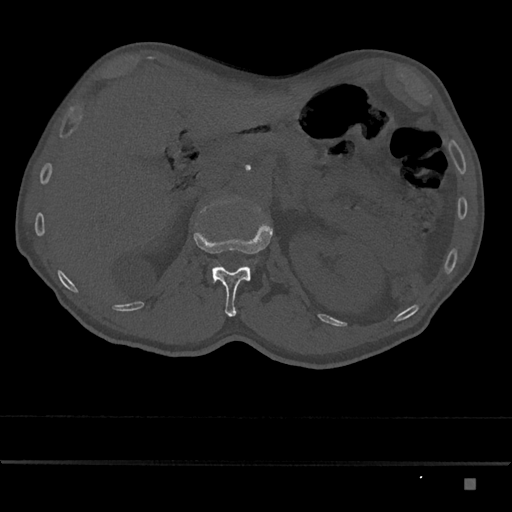
CT including the spine, one axial slice; slice 530 of 797 in the series (ordered by position); 120 kVp; bone window (W 1800 / L 400 HU); 0.5 mm slice thickness; 512 × 512 image matrix, field of view 390 × 390 mm. Patient: male, 72 years. From the clinical record (not read from this slice): primary cancer: prostate.
Outlined on this slice (semi-automatic segmentation, software-assisted and operator-edited):
- L1 vertebra: bounding box [x1, y1, x2, y2] px = [193, 222, 273, 317]